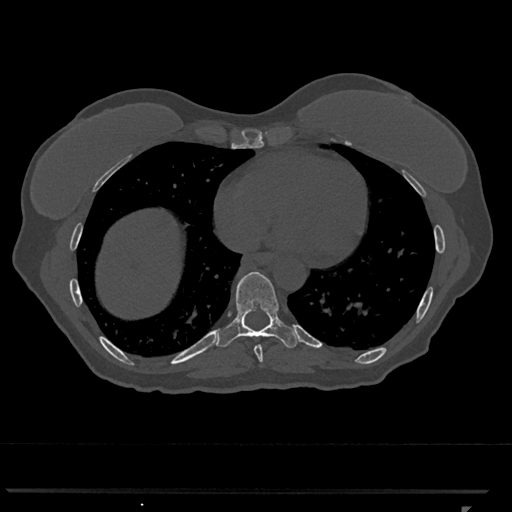
CT including the spine, one axial slice. Slice 627 of 793 in the series (ordered by position). Bone window (W 1800 / L 400 HU). 0.5 mm slice thickness. 512 × 512 image matrix, field of view 380 × 380 mm. Patient: female, 62 years. Case-level facts recorded for this patient, not image findings: primary cancer: renal.
Annotated regions visible in this slice (semi-automatically segmented with operator editing):
- T8 vertebra: bounding box [x1, y1, x2, y2] px = [254, 344, 263, 362]
- T9 vertebra: [215, 271, 299, 348]